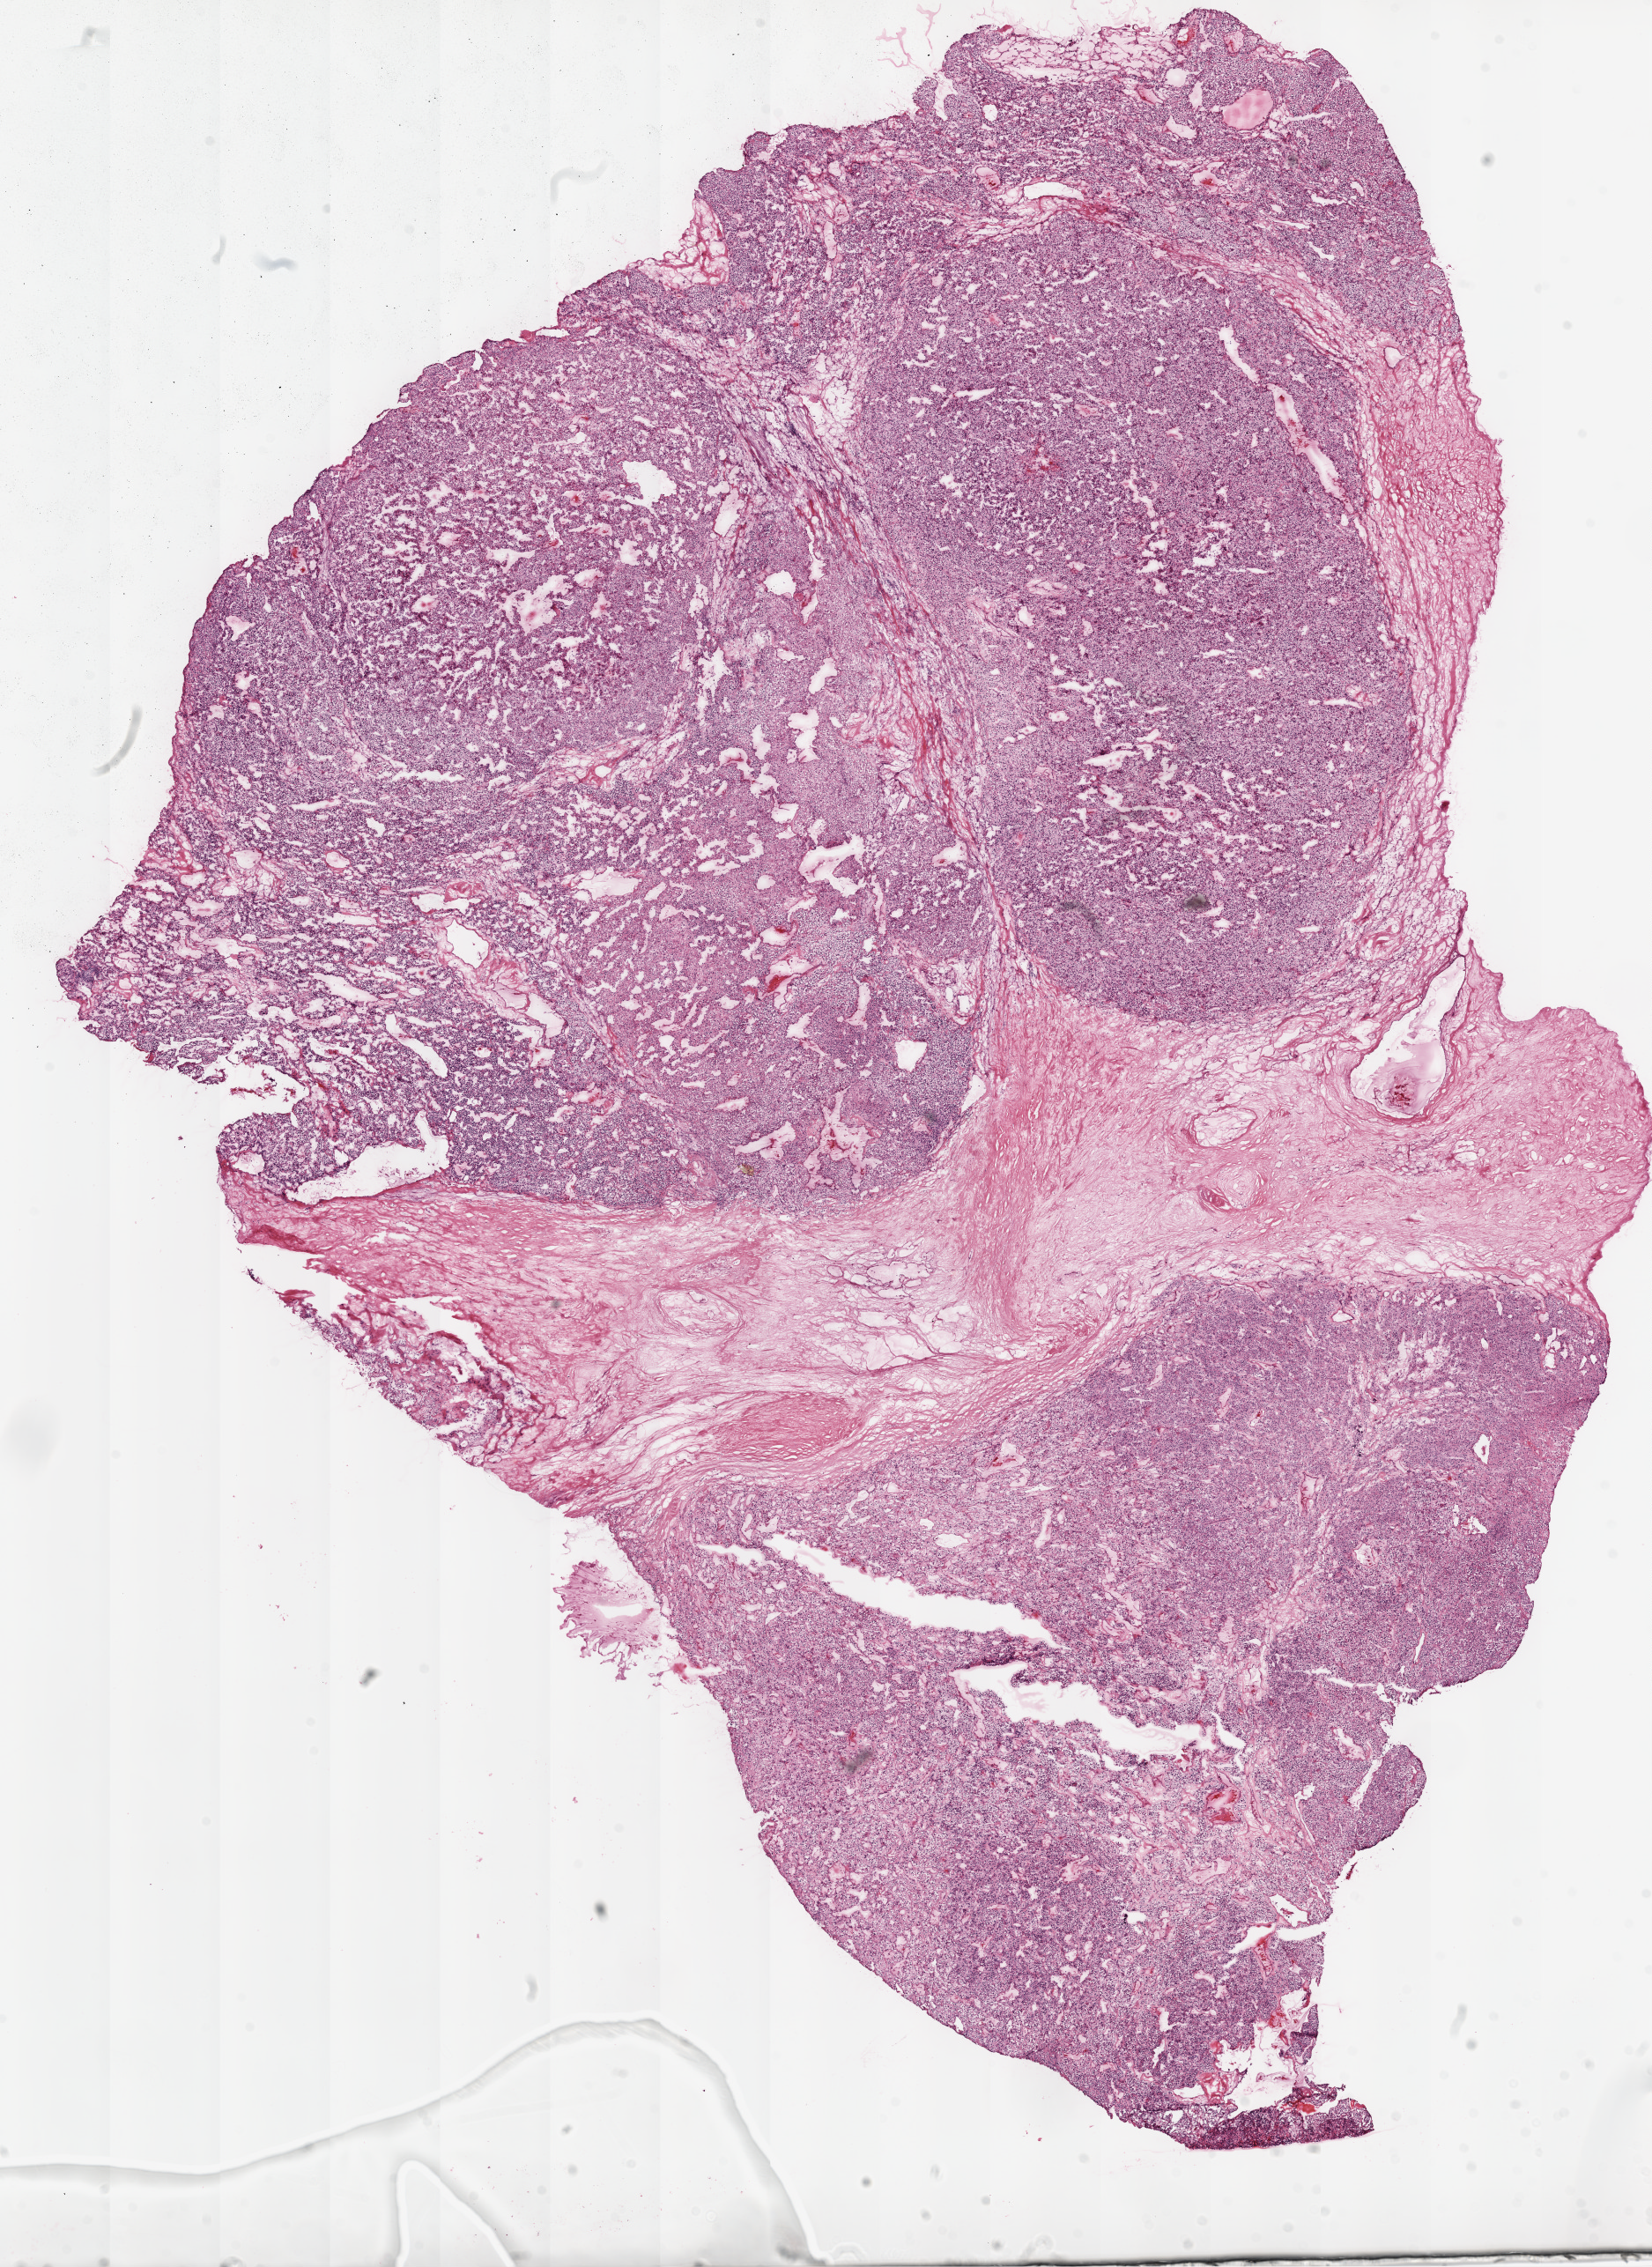
Hematoxylin and eosin (H&E) stained whole-slide image — shown as a low-resolution overview of the whole scanned area (about 15.0 x 20.6 mm, slide scanned at 20x). Frozen section from the top of the tissue portion. Kidney, primary tumour sample. Female, age 76 years at initial diagnosis. Histologic grade: G2 (moderately differentiated). Pathologist review of this section (percent, as recorded): tumour cells 75%, tumour nuclei 85%, normal cells 0%, stromal cells 25%, necrosis 0%.
- diagnosis: Clear cell adenocarcinoma, NOS
- laterality: left
- TNM: T3b NX M0
- AJCC pathologic stage: III